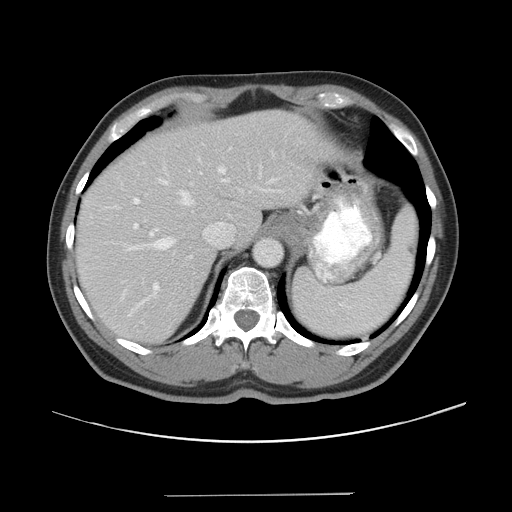
Contrast-enhanced abdominal CT, one axial slice; slice 31 of 43 in the series (ordered by position); intravenous contrast given; soft-tissue window (W 400 / L 40 HU); 512 × 512 image matrix. Male patient, age 65 years. From the clinical record (not read from this slice): diagnosis: colorectal cancer liver metastases, imaged before liver resection; multiple liver metastases: no; largest metastasis: 3.8 cm; disease in both lobes: no.
Structures marked on this image (expert manual segmentation):
- hepatic veins: bounding box <139,168,225,250> (left, top, right, bottom; pixels)
- liver: <77,112,325,342>
- planned liver remnant (the part of the liver to remain after resection): <77,112,325,340>
- portal vein (with intrahepatic branches): <130,149,286,315>